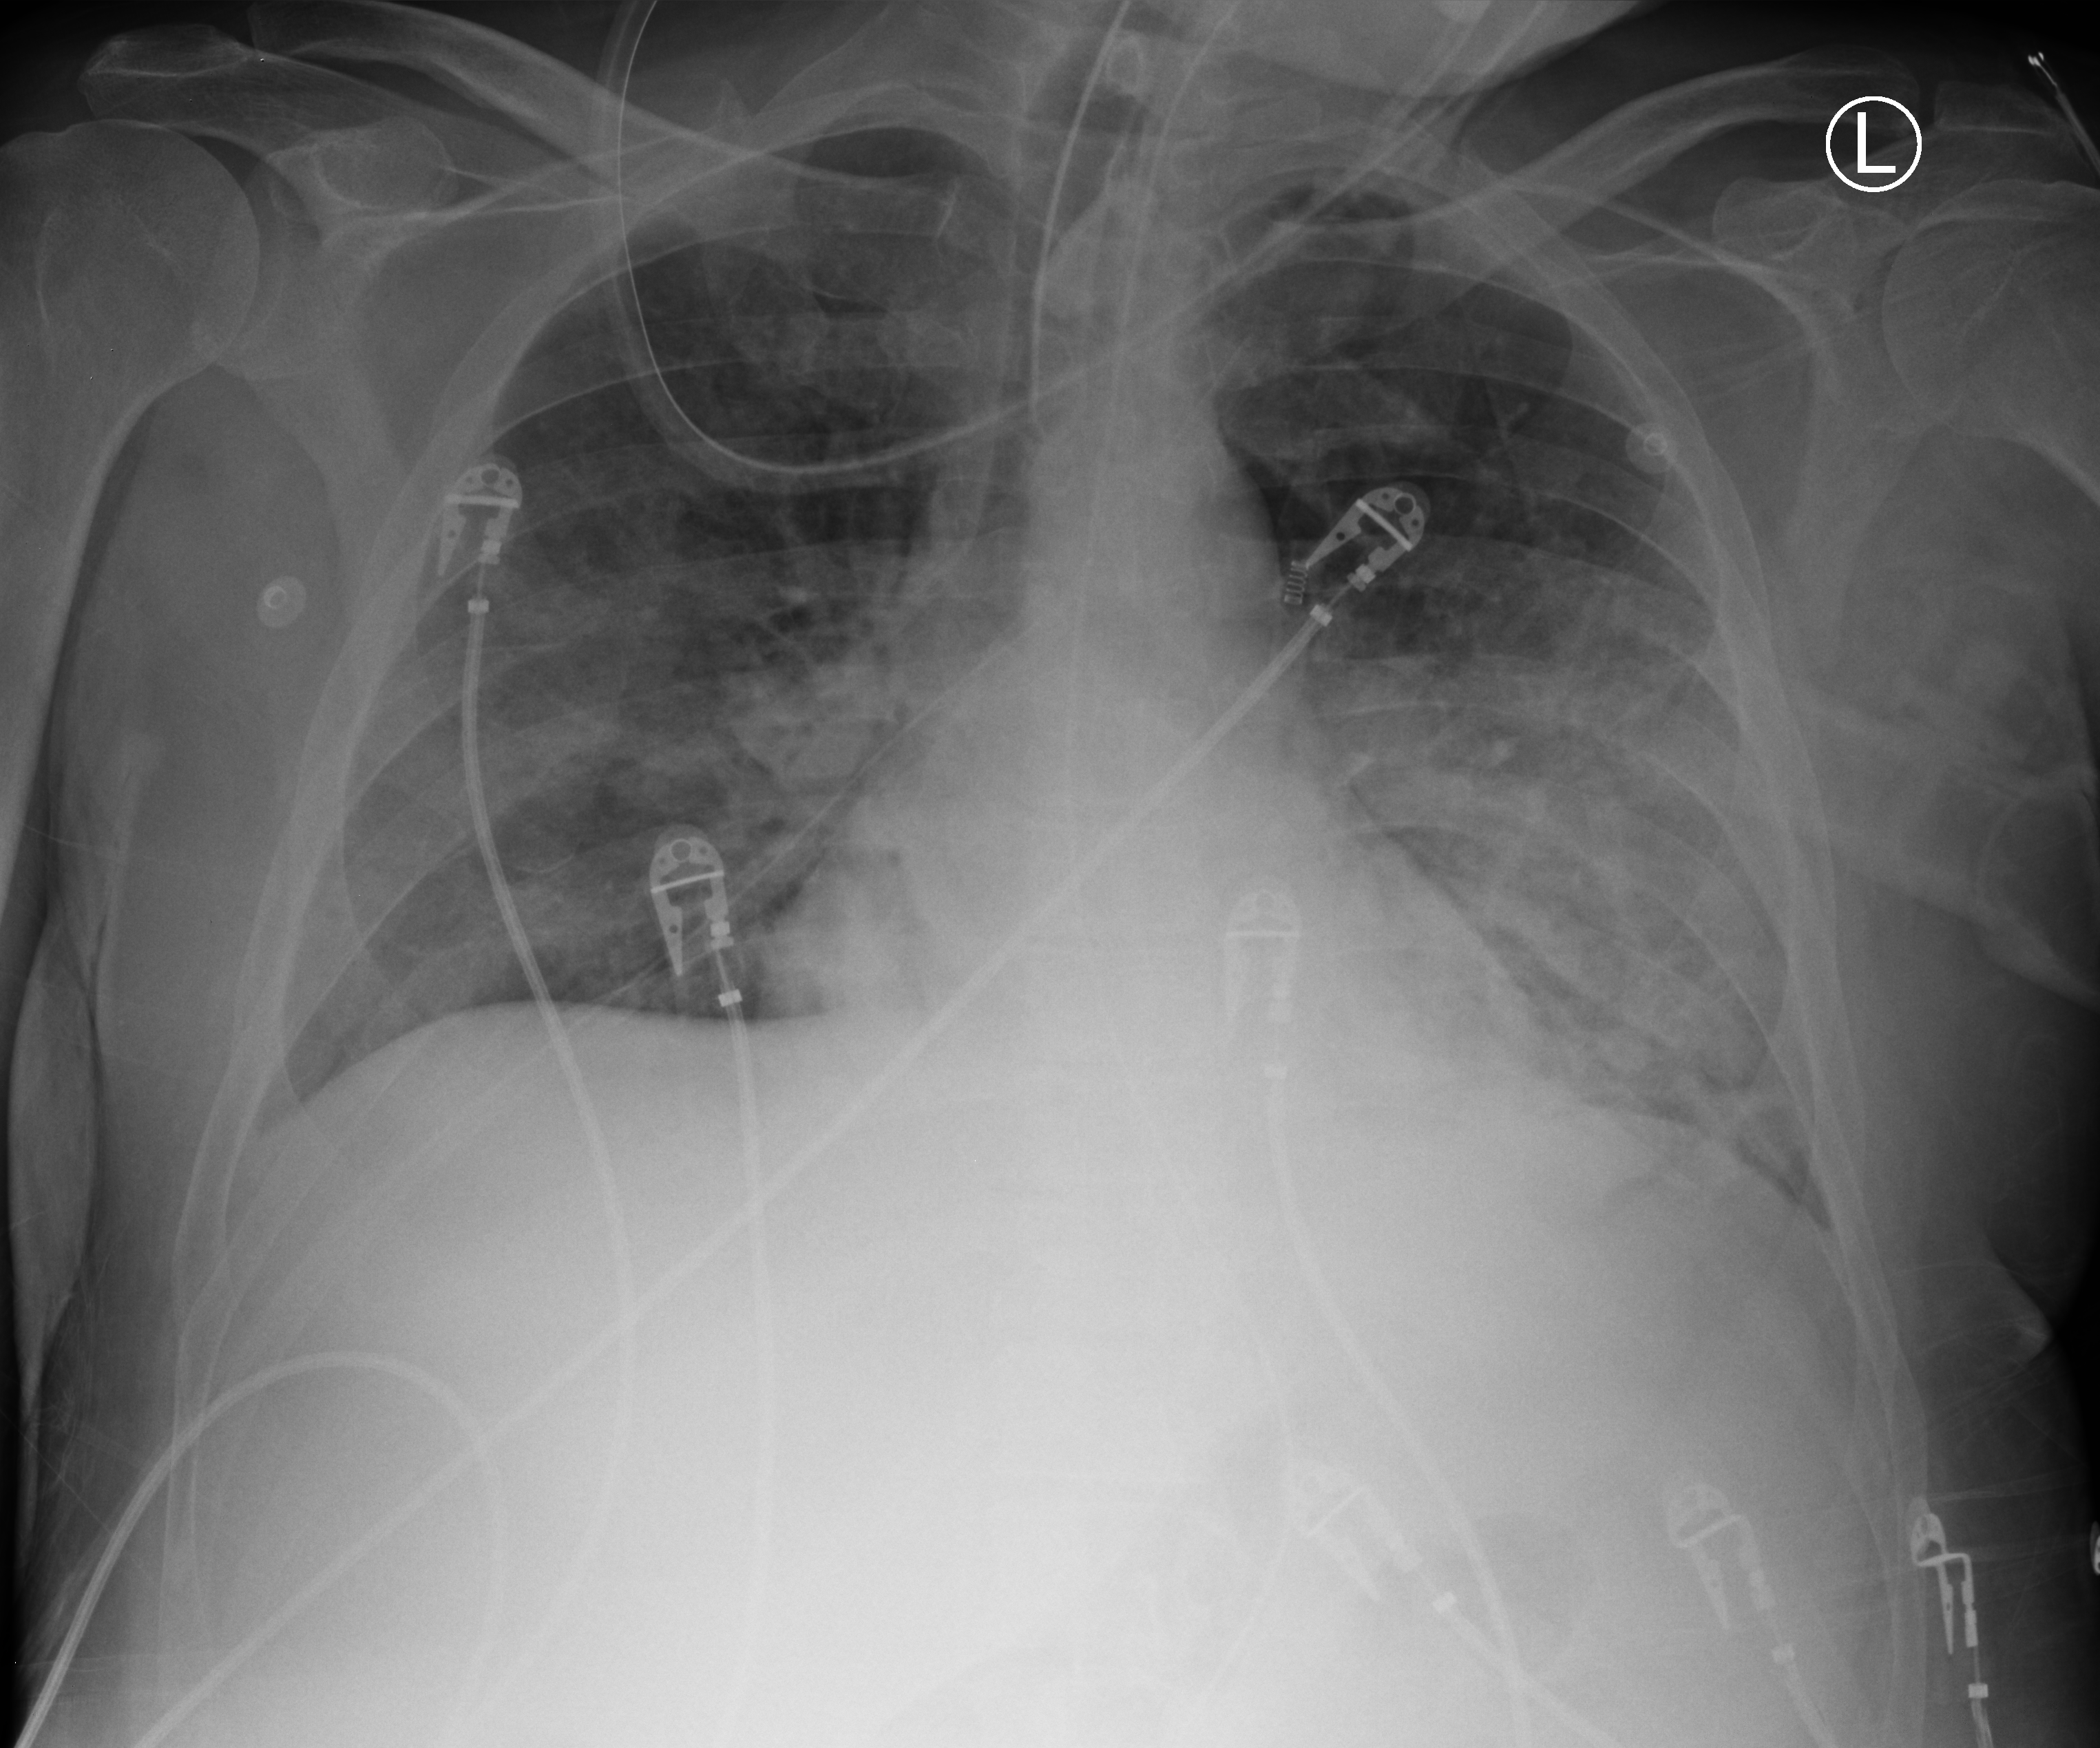
Portable chest radiograph. Patient hospitalised with COVID-19; male, aged 18–59 years.
Admission-level facts for this patient (not findings on this image; timing relative to this image not recorded): mechanically ventilated during this hospital stay: yes; admitted to intensive care during this hospital stay: yes; COPD (admission record): no.